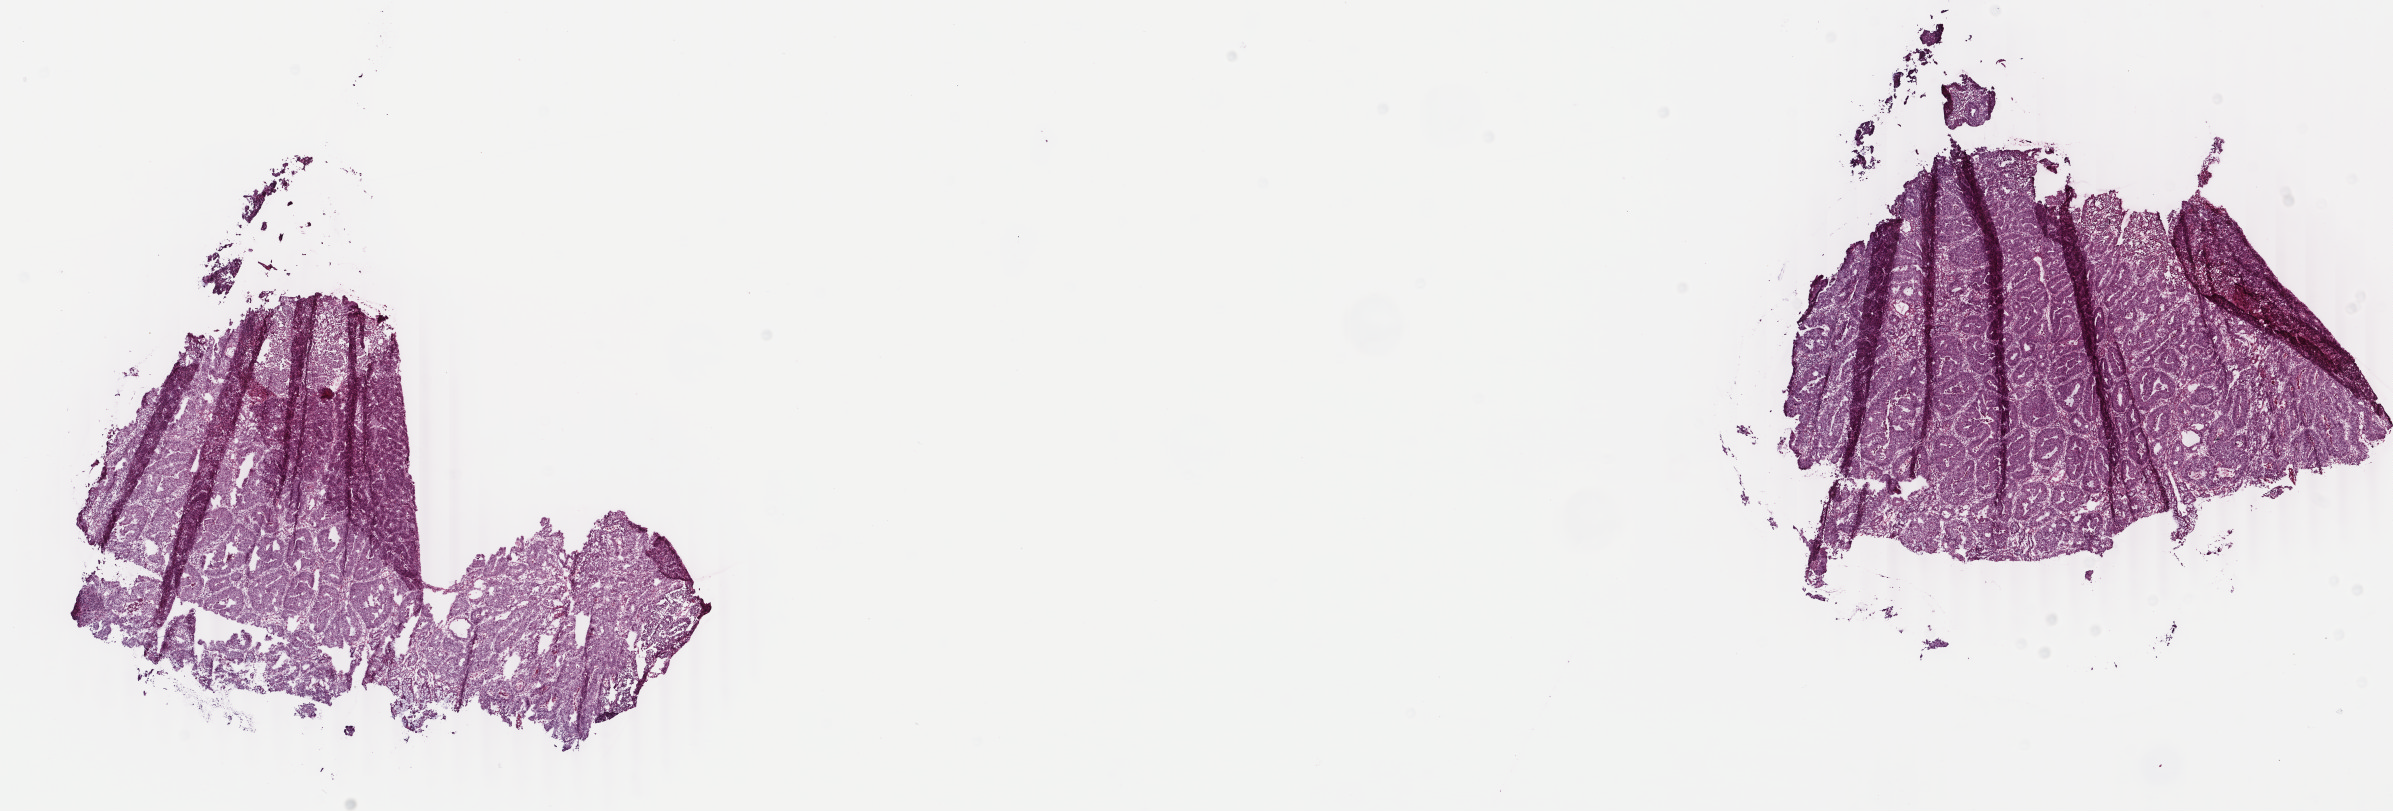
H&E whole-slide image — low-resolution overview of the scanned area, about 19.0 x 6.5 mm (acquisition: 40x scan); frozen section from the bottom of the tissue portion; sample: primary tumour, rectum. Patient: male, age at initial diagnosis 68 years. Pathologist review of this section (percent, as recorded): tumour cells 88%, tumour nuclei 90%, normal cells 3%, stromal cells 6%, necrosis 3%. Inflammatory infiltration, as recorded: lymphocyte infiltration 25%, monocyte infiltration 2%, neutrophil infiltration 20%.
* AJCC pathologic stage: IIA
* lymph nodes positive (case pathology): 0 of 31 examined
* diagnosis: Adenocarcinoma, NOS